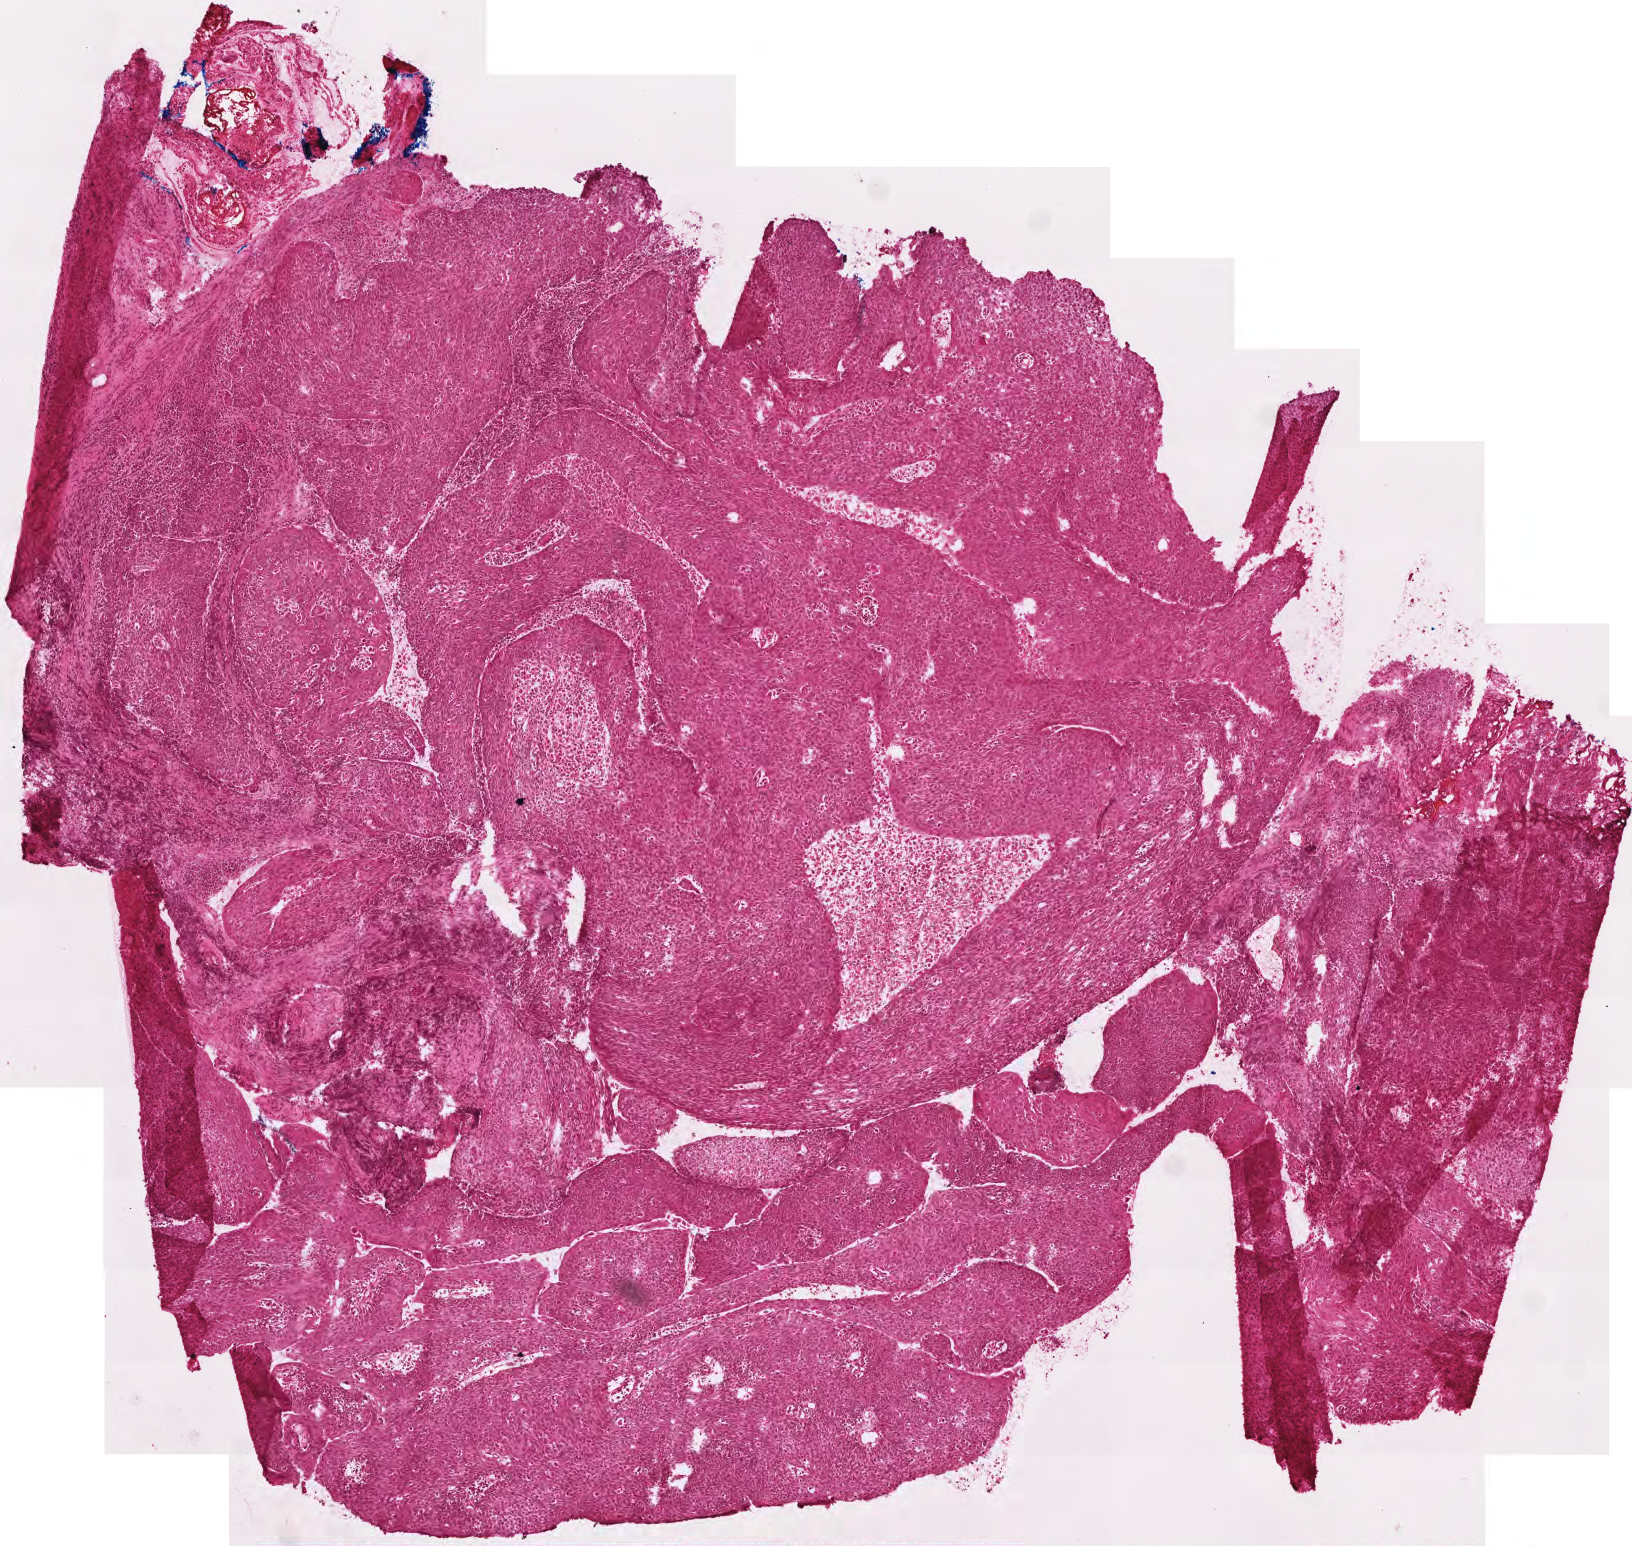
Whole-slide histology image, H&E-stained — a low-resolution overview of the entire scanned area, about 3.3 x 3.1 mm. Frozen section from the top of the tissue portion. Head and neck, primary tumour sample. Male, age 42 years at initial diagnosis.
Diagnosis: Squamous cell carcinoma, NOS (tonsil, NOS).